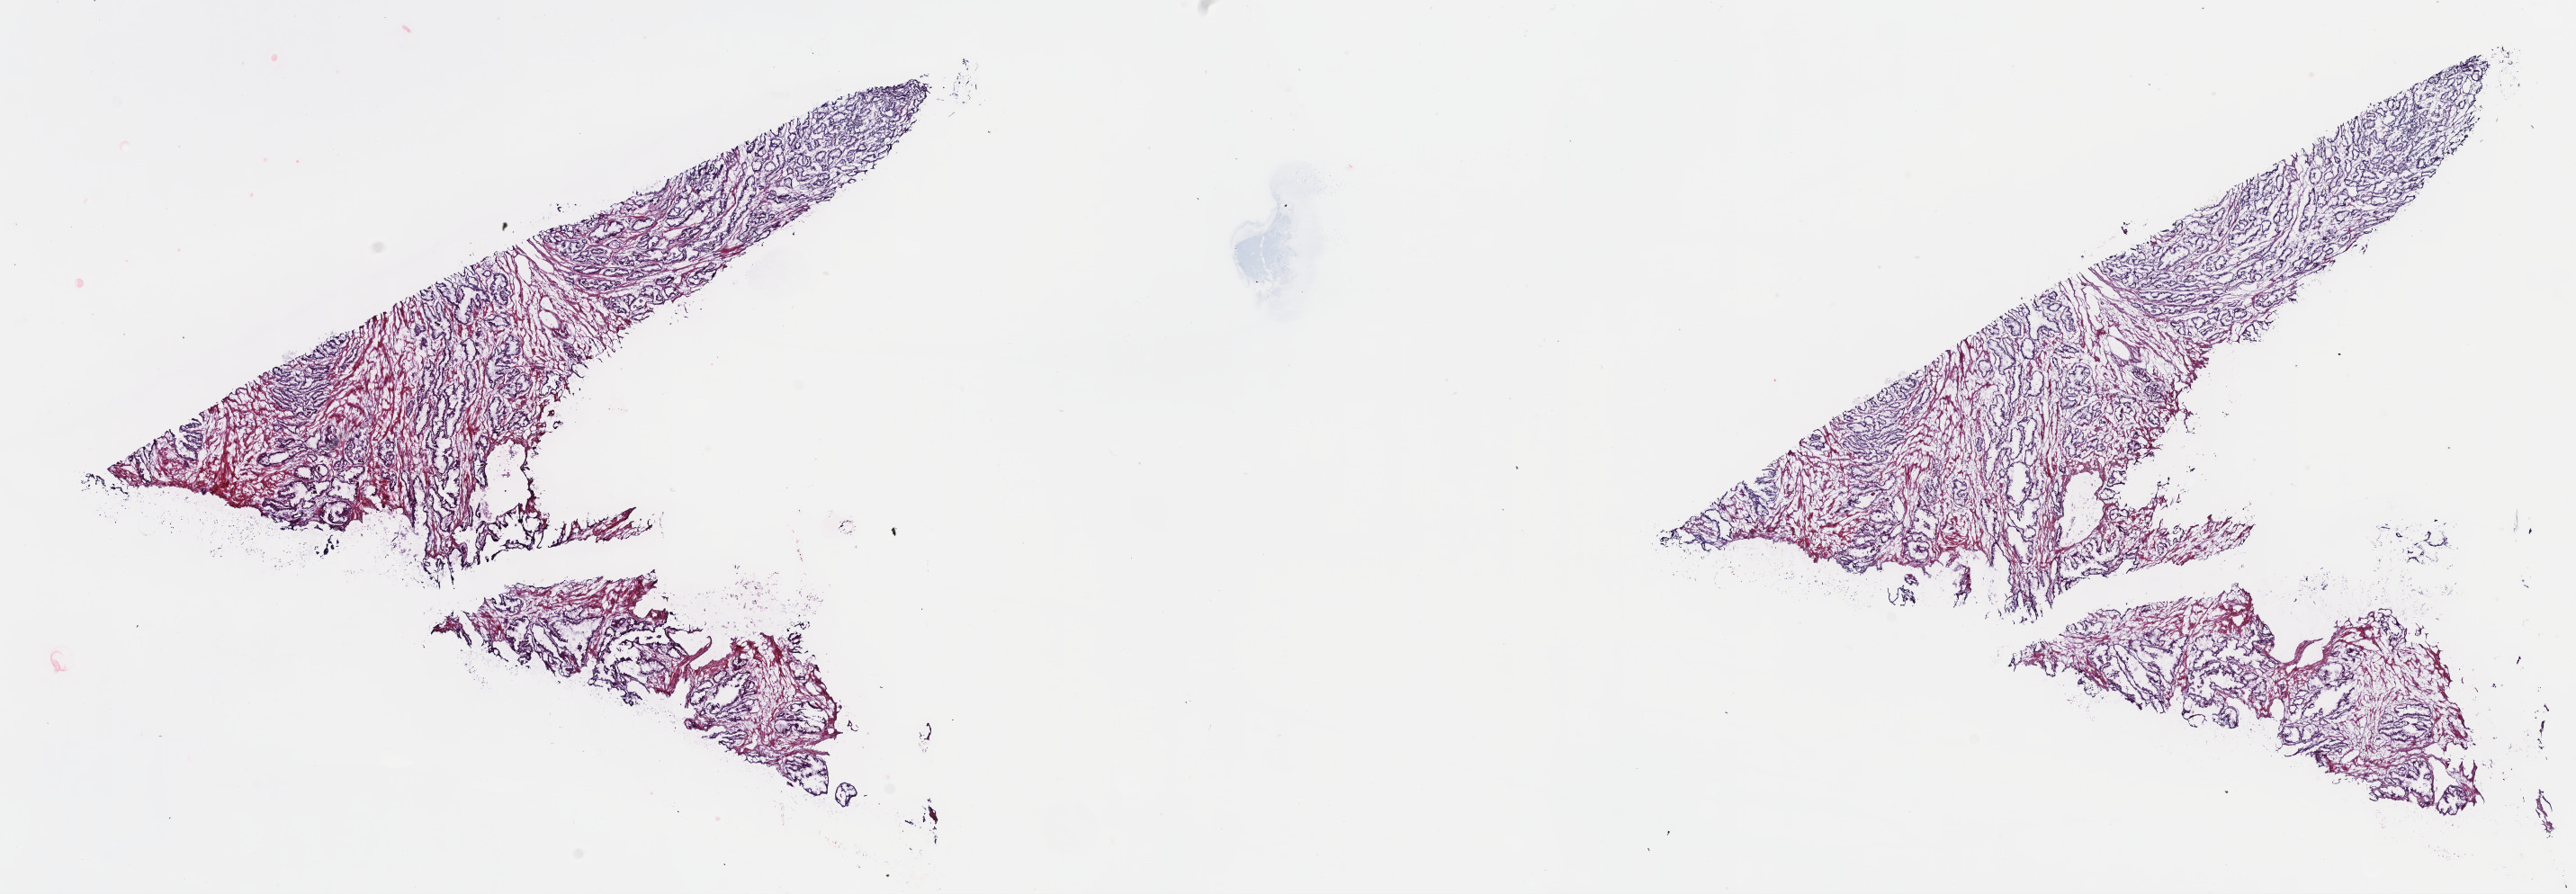
H&E whole-slide image, whole scanned area (about 23.2 x 8.0 mm) shown as a low-resolution overview; frozen section; sample: primary tumour, prostate. Male patient; age at initial diagnosis 51 years. Gleason score: 6 (3+3). Slide review estimates, as recorded: tumour cells 58%, tumour nuclei 90%, normal cells 2%, stromal cells 38%, necrosis 2%. Infiltration values recorded for this section: lymphocyte infiltration 4%, monocyte infiltration 0%, neutrophil infiltration 0%.
Diagnosis: Adenocarcinoma, NOS. Lymph nodes positive (case pathology): 0 of 15 examined. Laterality: bilateral.